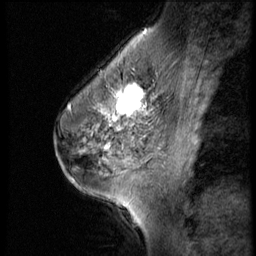
Breast MRI (dynamic contrast-enhanced), one sagittal slice; 3 images stored at this slice position (order not interpretable as contrast timing); 1.5 T; TE 4.2 ms, TR 9 ms; 2.5 mm slice thickness; 256 × 256 image matrix. Female patient, age 45 years. From the clinical record (not read from this slice): setting: breast cancer imaged before/during neoadjuvant chemotherapy; receptor status: HR-positive, HER2-negative.
Structures marked on this image (semi-automatic segmentation, software-assisted and operator-edited):
- analysis volume of interest (the breast-tissue region the enhancement analysis was run in; not a lesion): box from (x=102, y=77) to (x=166, y=129) px
- tumour enhancement mask (voxels above the 140 % enhancement threshold inside the analysis volume of interest): (x=102, y=83)–(x=157, y=129)